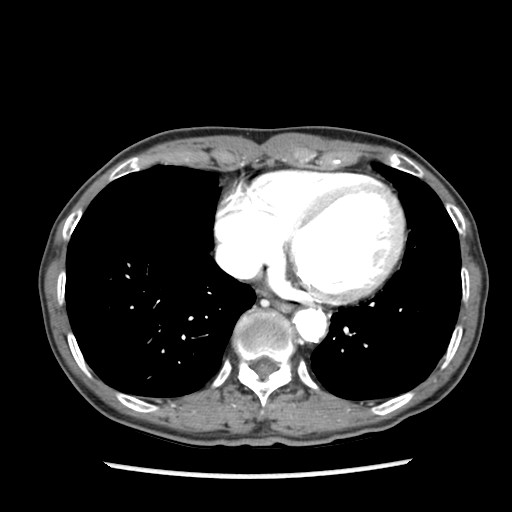
Contrast-enhanced abdominal CT (liver protocol), one axial slice; slice 82 of 87 in the series (ordered by position); reconstruction kernel STANDARD; 140 kVp; soft-tissue window (W 400 / L 40 HU); 2.5 mm slice thickness; 512 × 512 image matrix. Case-level facts recorded for this patient, not image findings: diagnosis: hepatocellular carcinoma (patient treated with transarterial chemoembolisation; whether this scan precedes or follows treatment is not stated here); TNM stage (as recorded): Stage-IIIB; Child-Pugh class: A; tumour differentiation: well differentiated; tumour nodularity: uninodular.
Outlined on this slice (semi-automatic segmentation, software-assisted and operator-edited):
- abdominal aorta: bounding box [x1, y1, x2, y2] px = [295, 308, 325, 341]